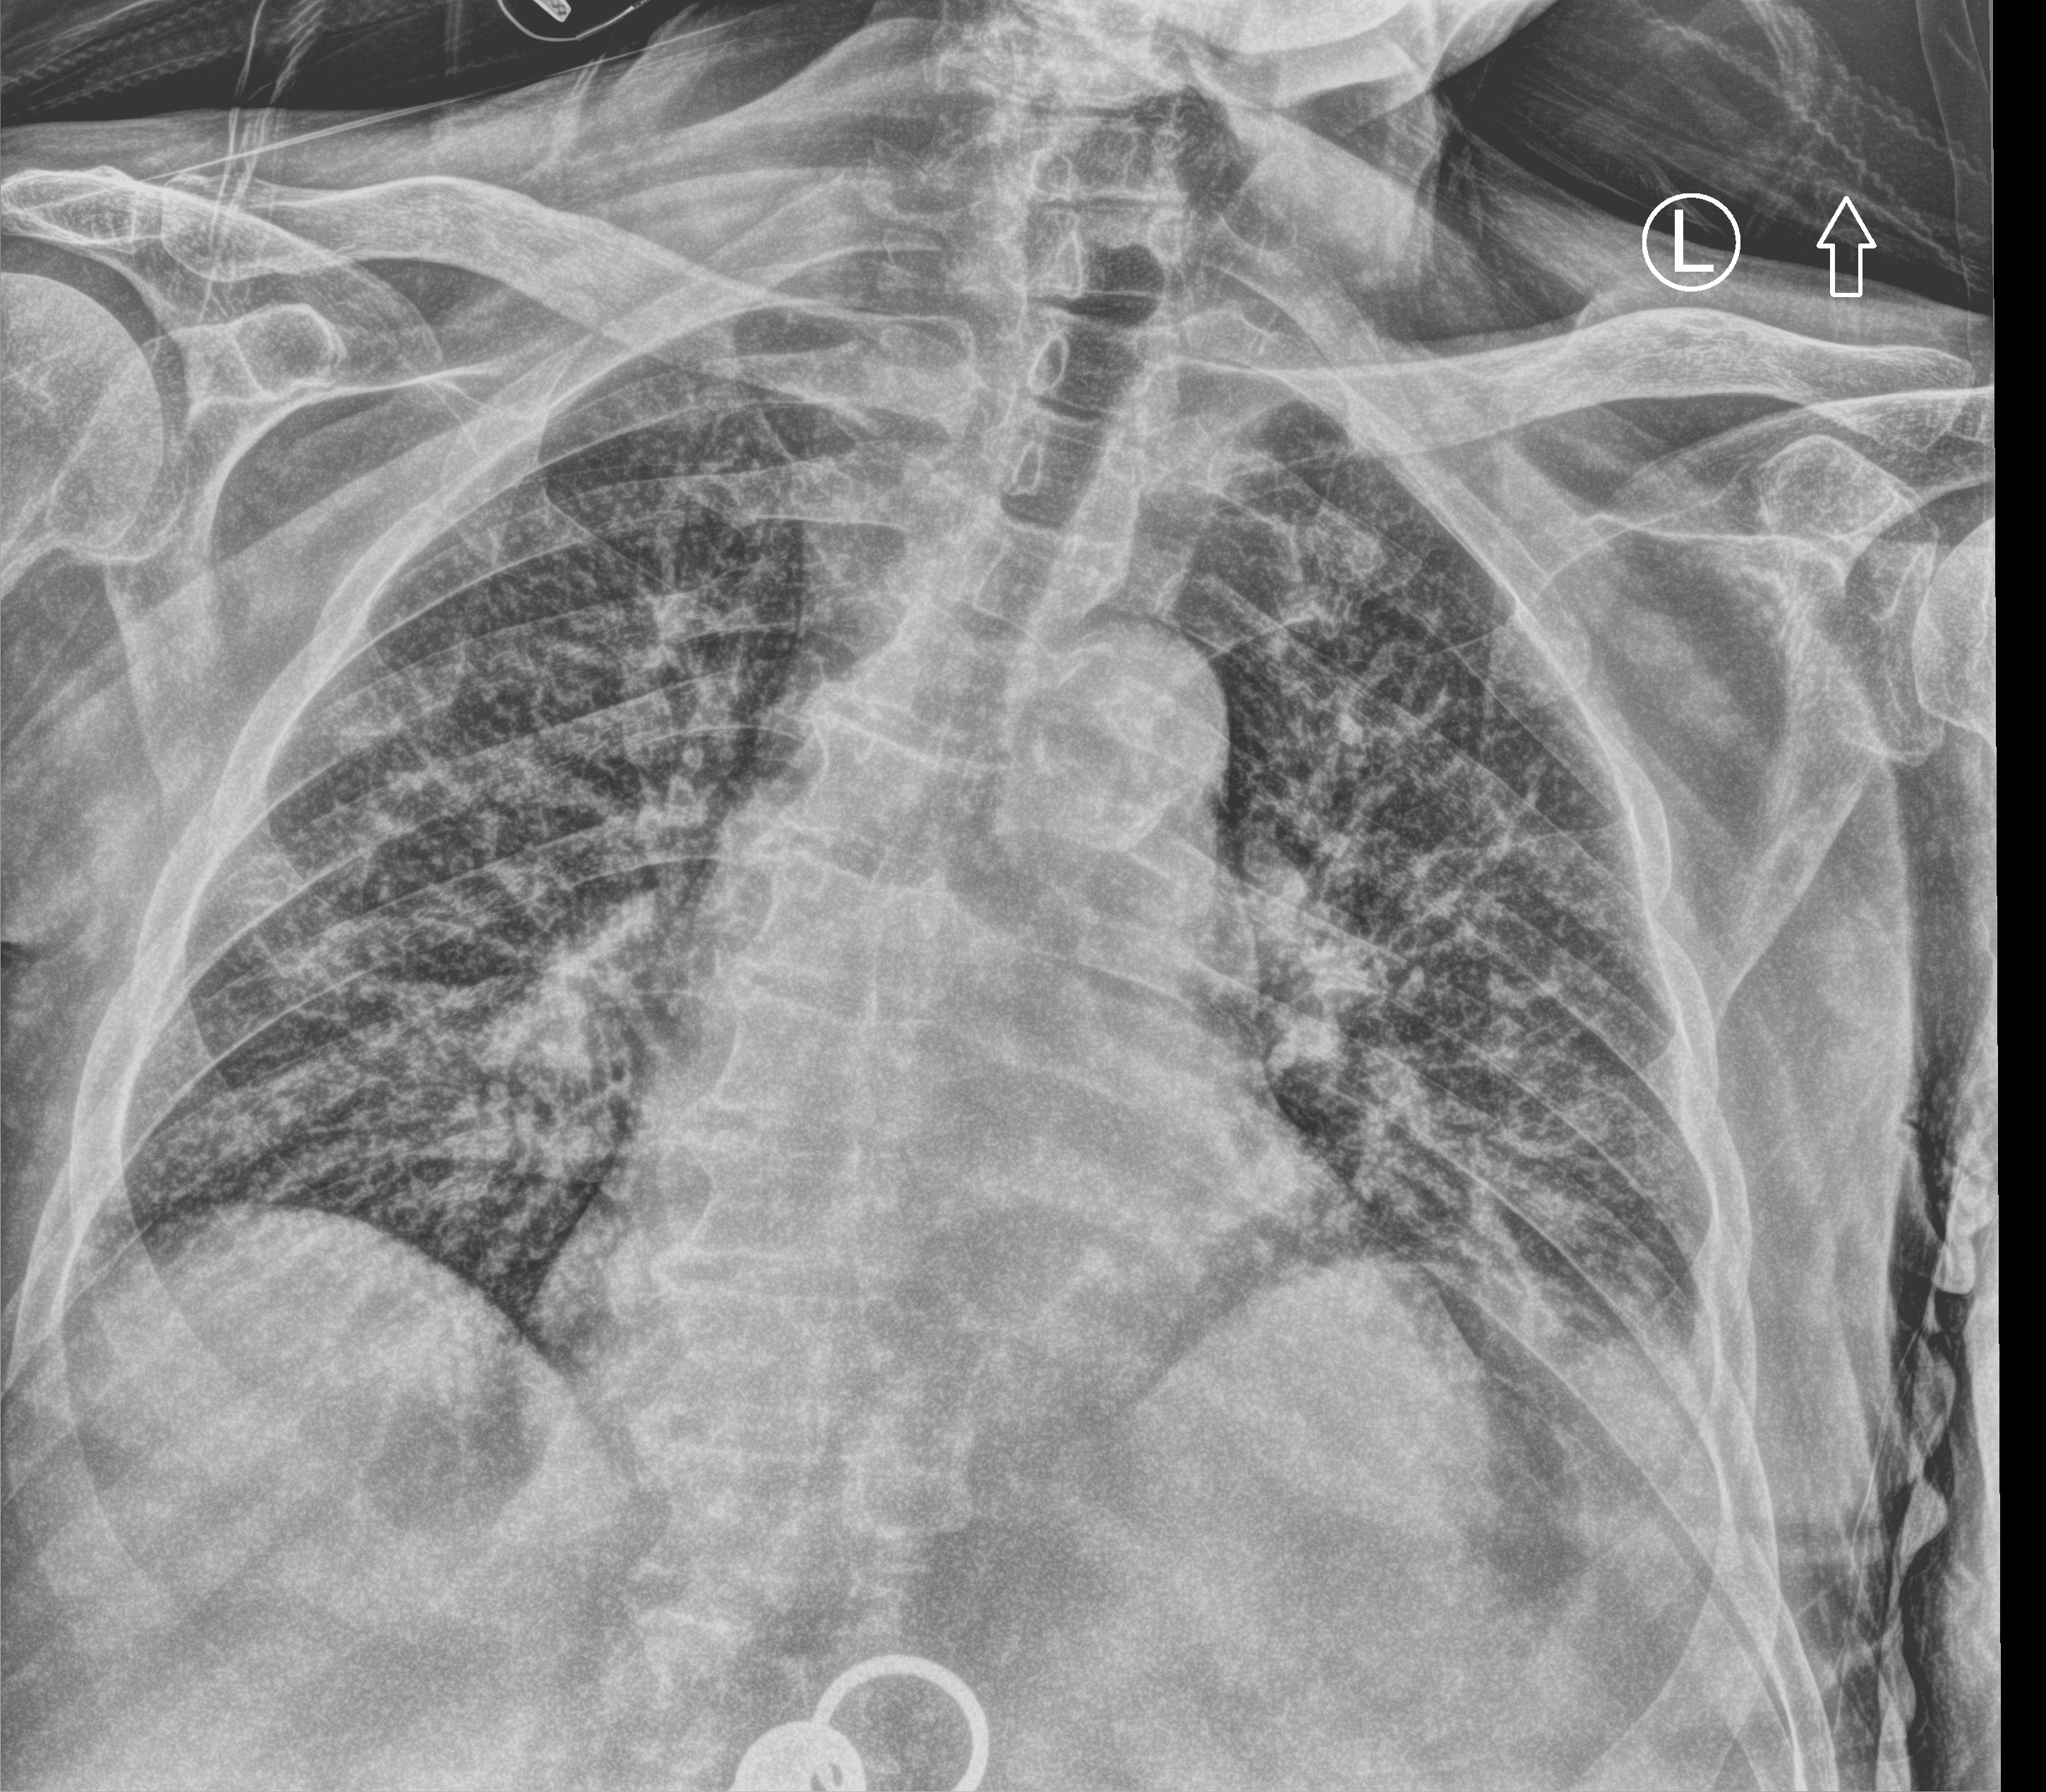
Bedside chest radiograph (computed radiography), anteroposterior (AP) projection. Male patient hospitalised with COVID-19, age 75–90 years.
From the hospital-stay record, not from the radiograph (when in the stay this image was taken is not recorded):
- mechanically ventilated during this hospital stay: no
- admitted to intensive care during this hospital stay: no